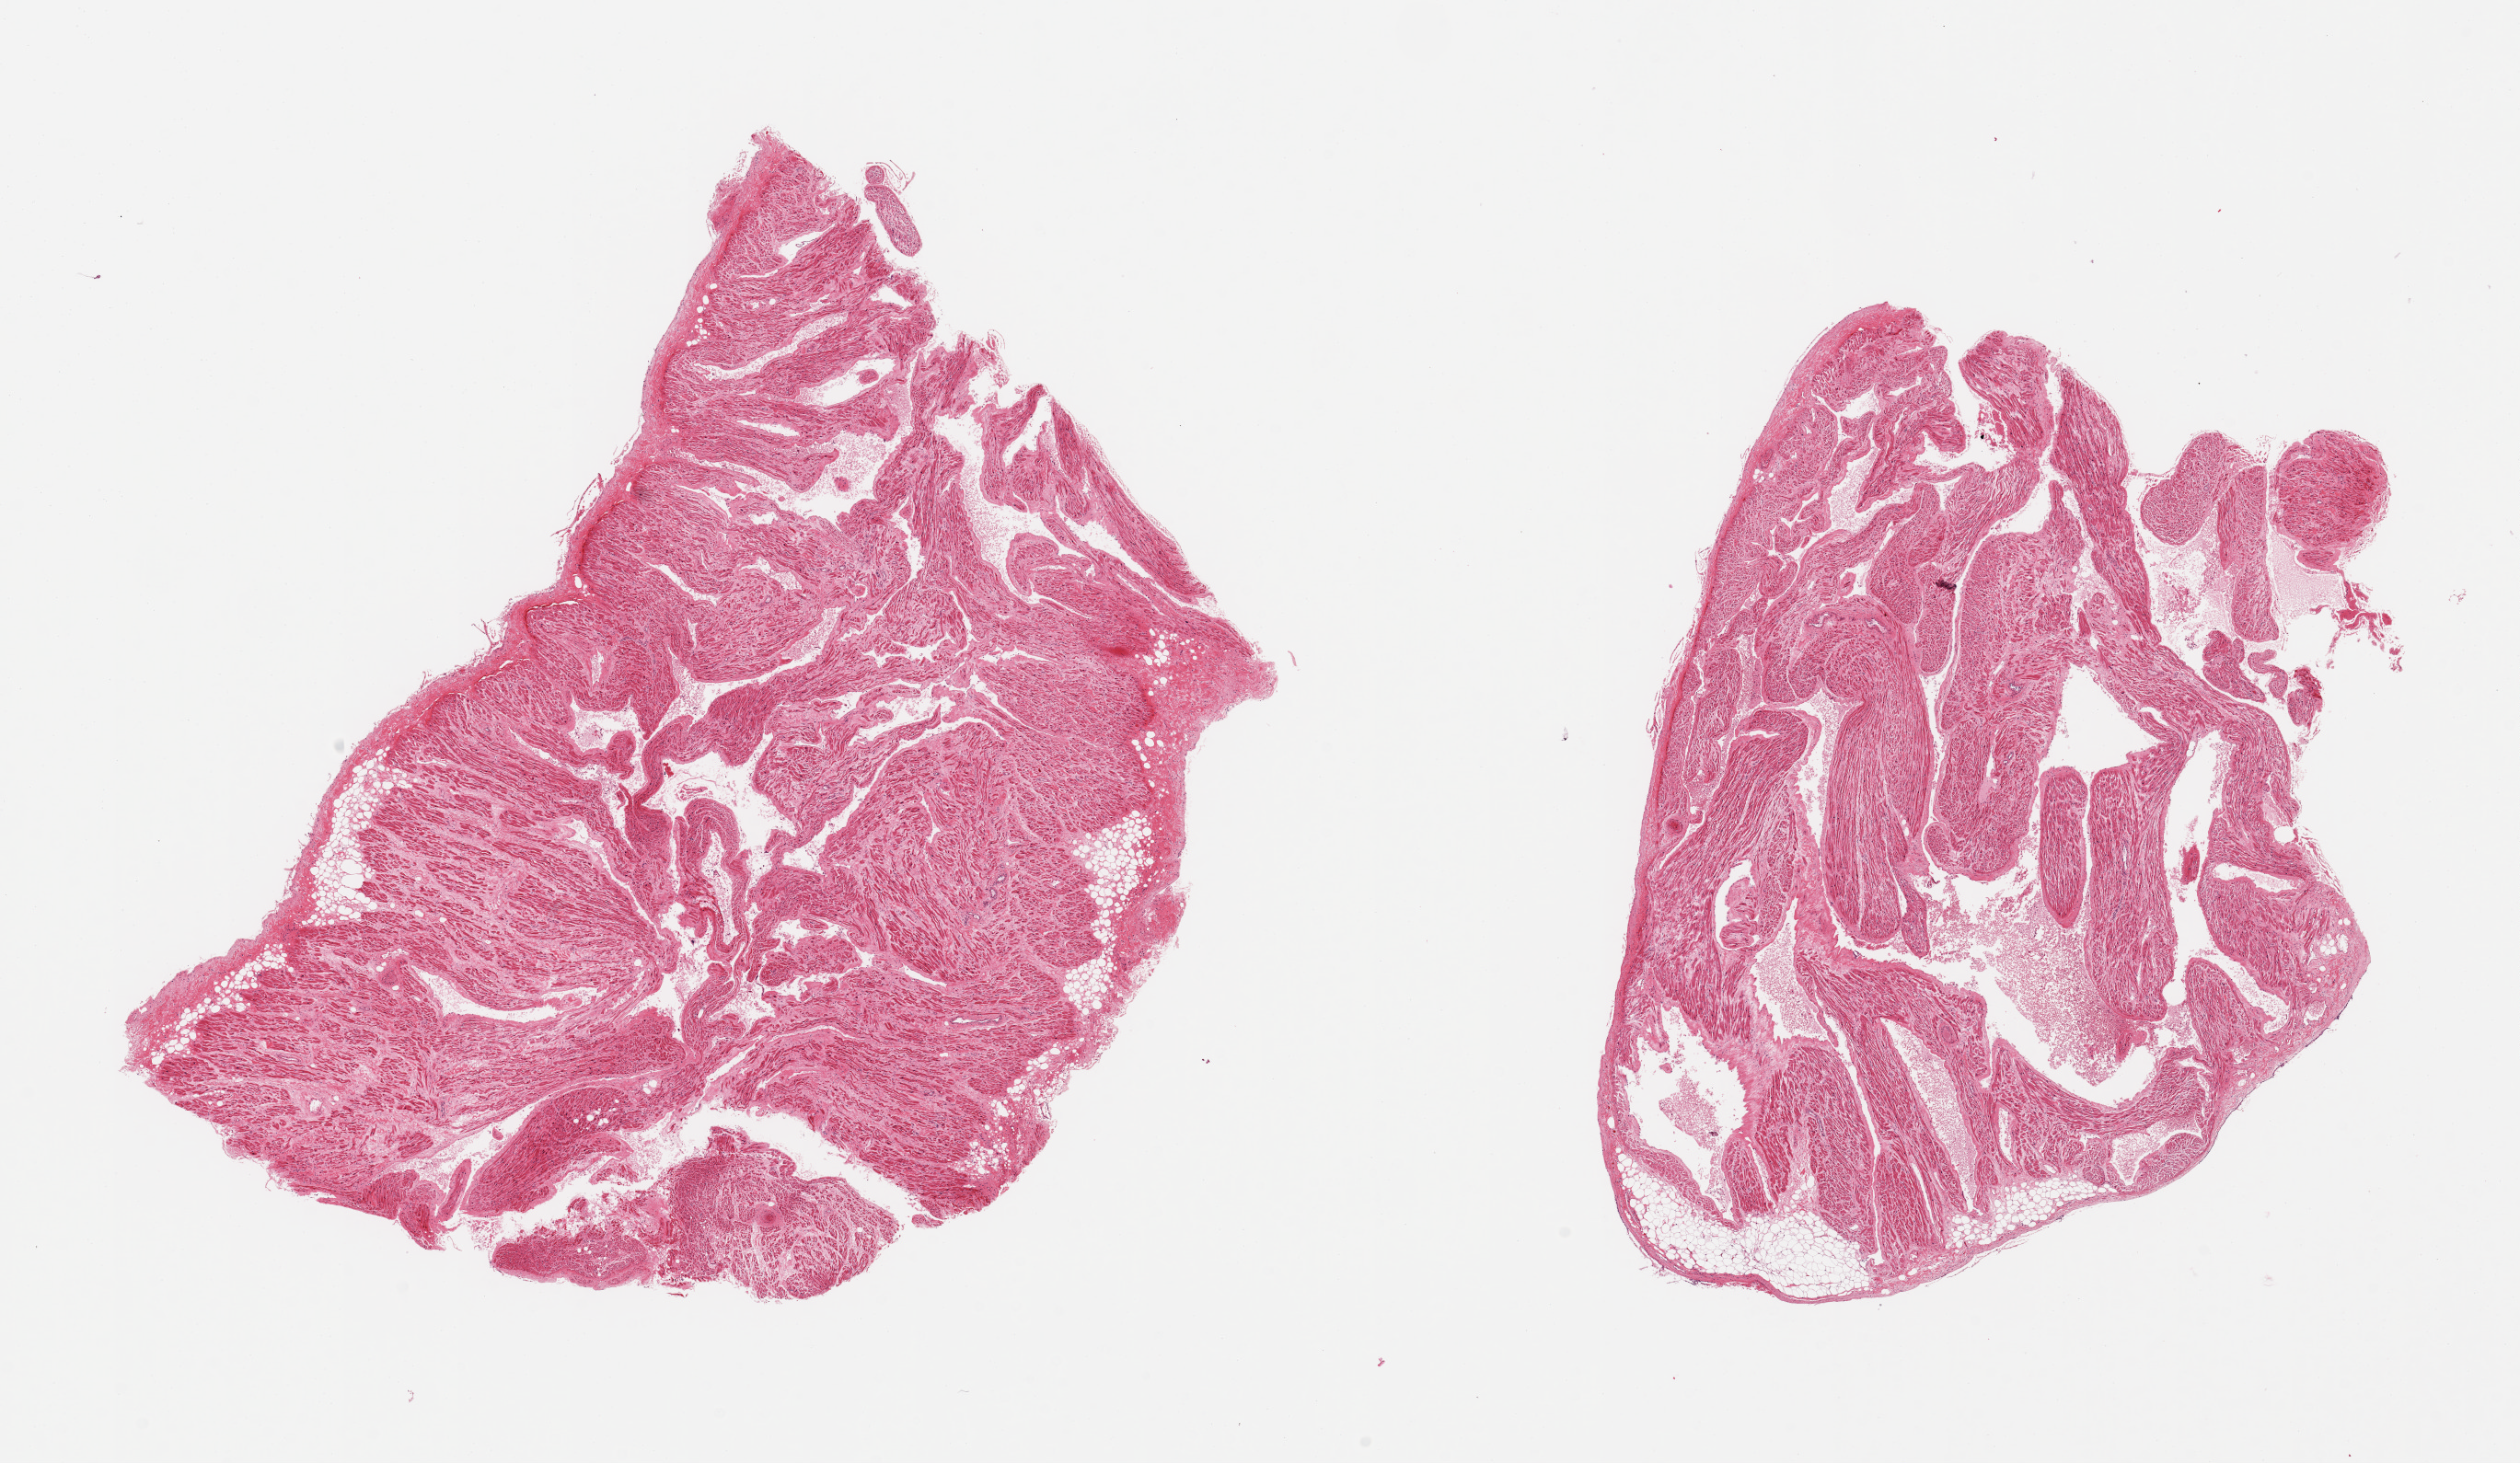
Digitized hematoxylin and eosin (H&E)-stained section, low-resolution overview of the scanned area, about 21.7 x 12.6 mm, PAXgene-fixed, paraffin-embedded tissue, sampled site (target tissue): auricular appendage, donor tissue sample. Donor: male.
Reviewer comment on this tissue sample: 2 pieces, no abnormalities.